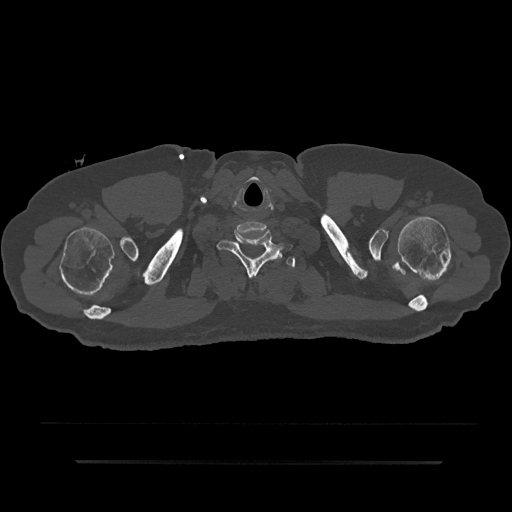
CT including the spine, one axial slice. Slice 773 of 797 in the series (ordered by position). Bone window (W 1800 / L 400 HU). 0.5 mm slice thickness. 512 × 512 image matrix. Patient: male, 59 years. From the clinical record (not read from this slice): primary cancer: bile ducts; vertebrae with lytic lesions (as recorded): T10.
Outlined on this slice (semi-automatic segmentation, software-assisted and operator-edited):
- T1 vertebra: bounding box [x1, y1, x2, y2] px = [274, 256, 296, 269]